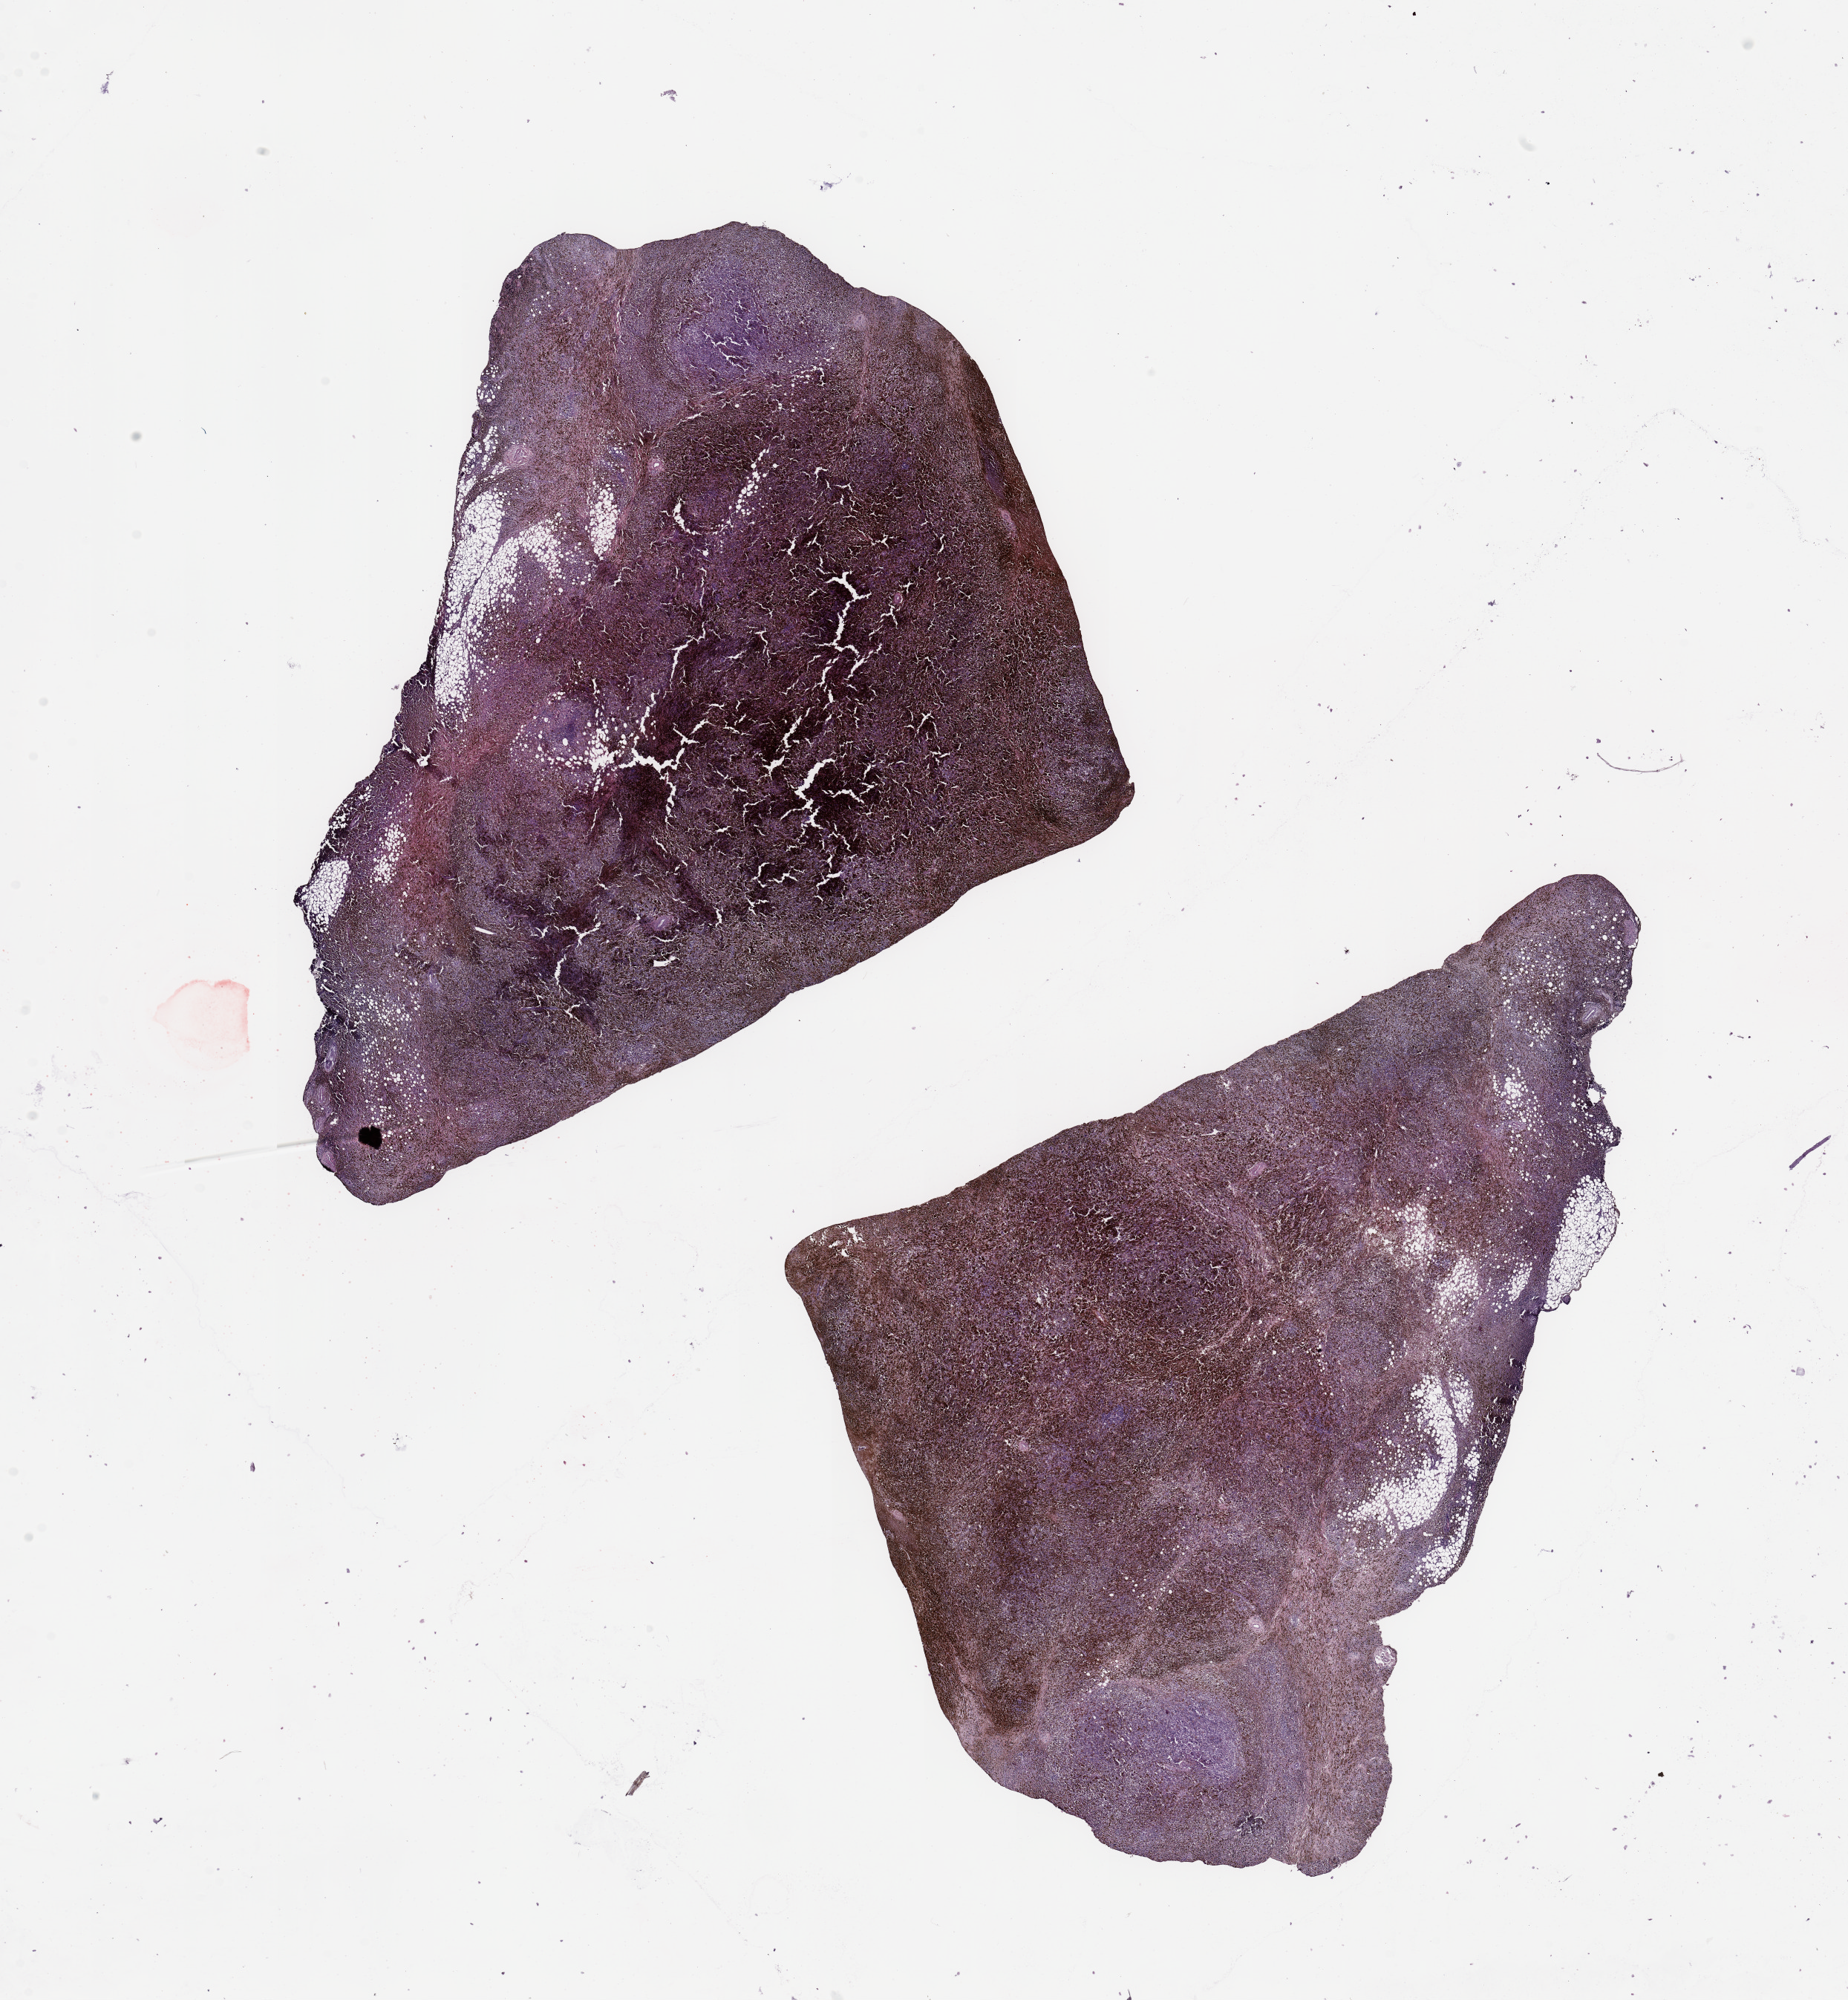
Digitized Hematoxylin and eosin (H&E) stained tissue section (whole slide) — low-resolution overview of the scanned area, about 19.7 x 21.3 mm (from a 20x scan), melanoma tumour tissue; sampled site not recorded. 64-year-old male patient.
Diagnosis: Malignant melanoma, NOS.